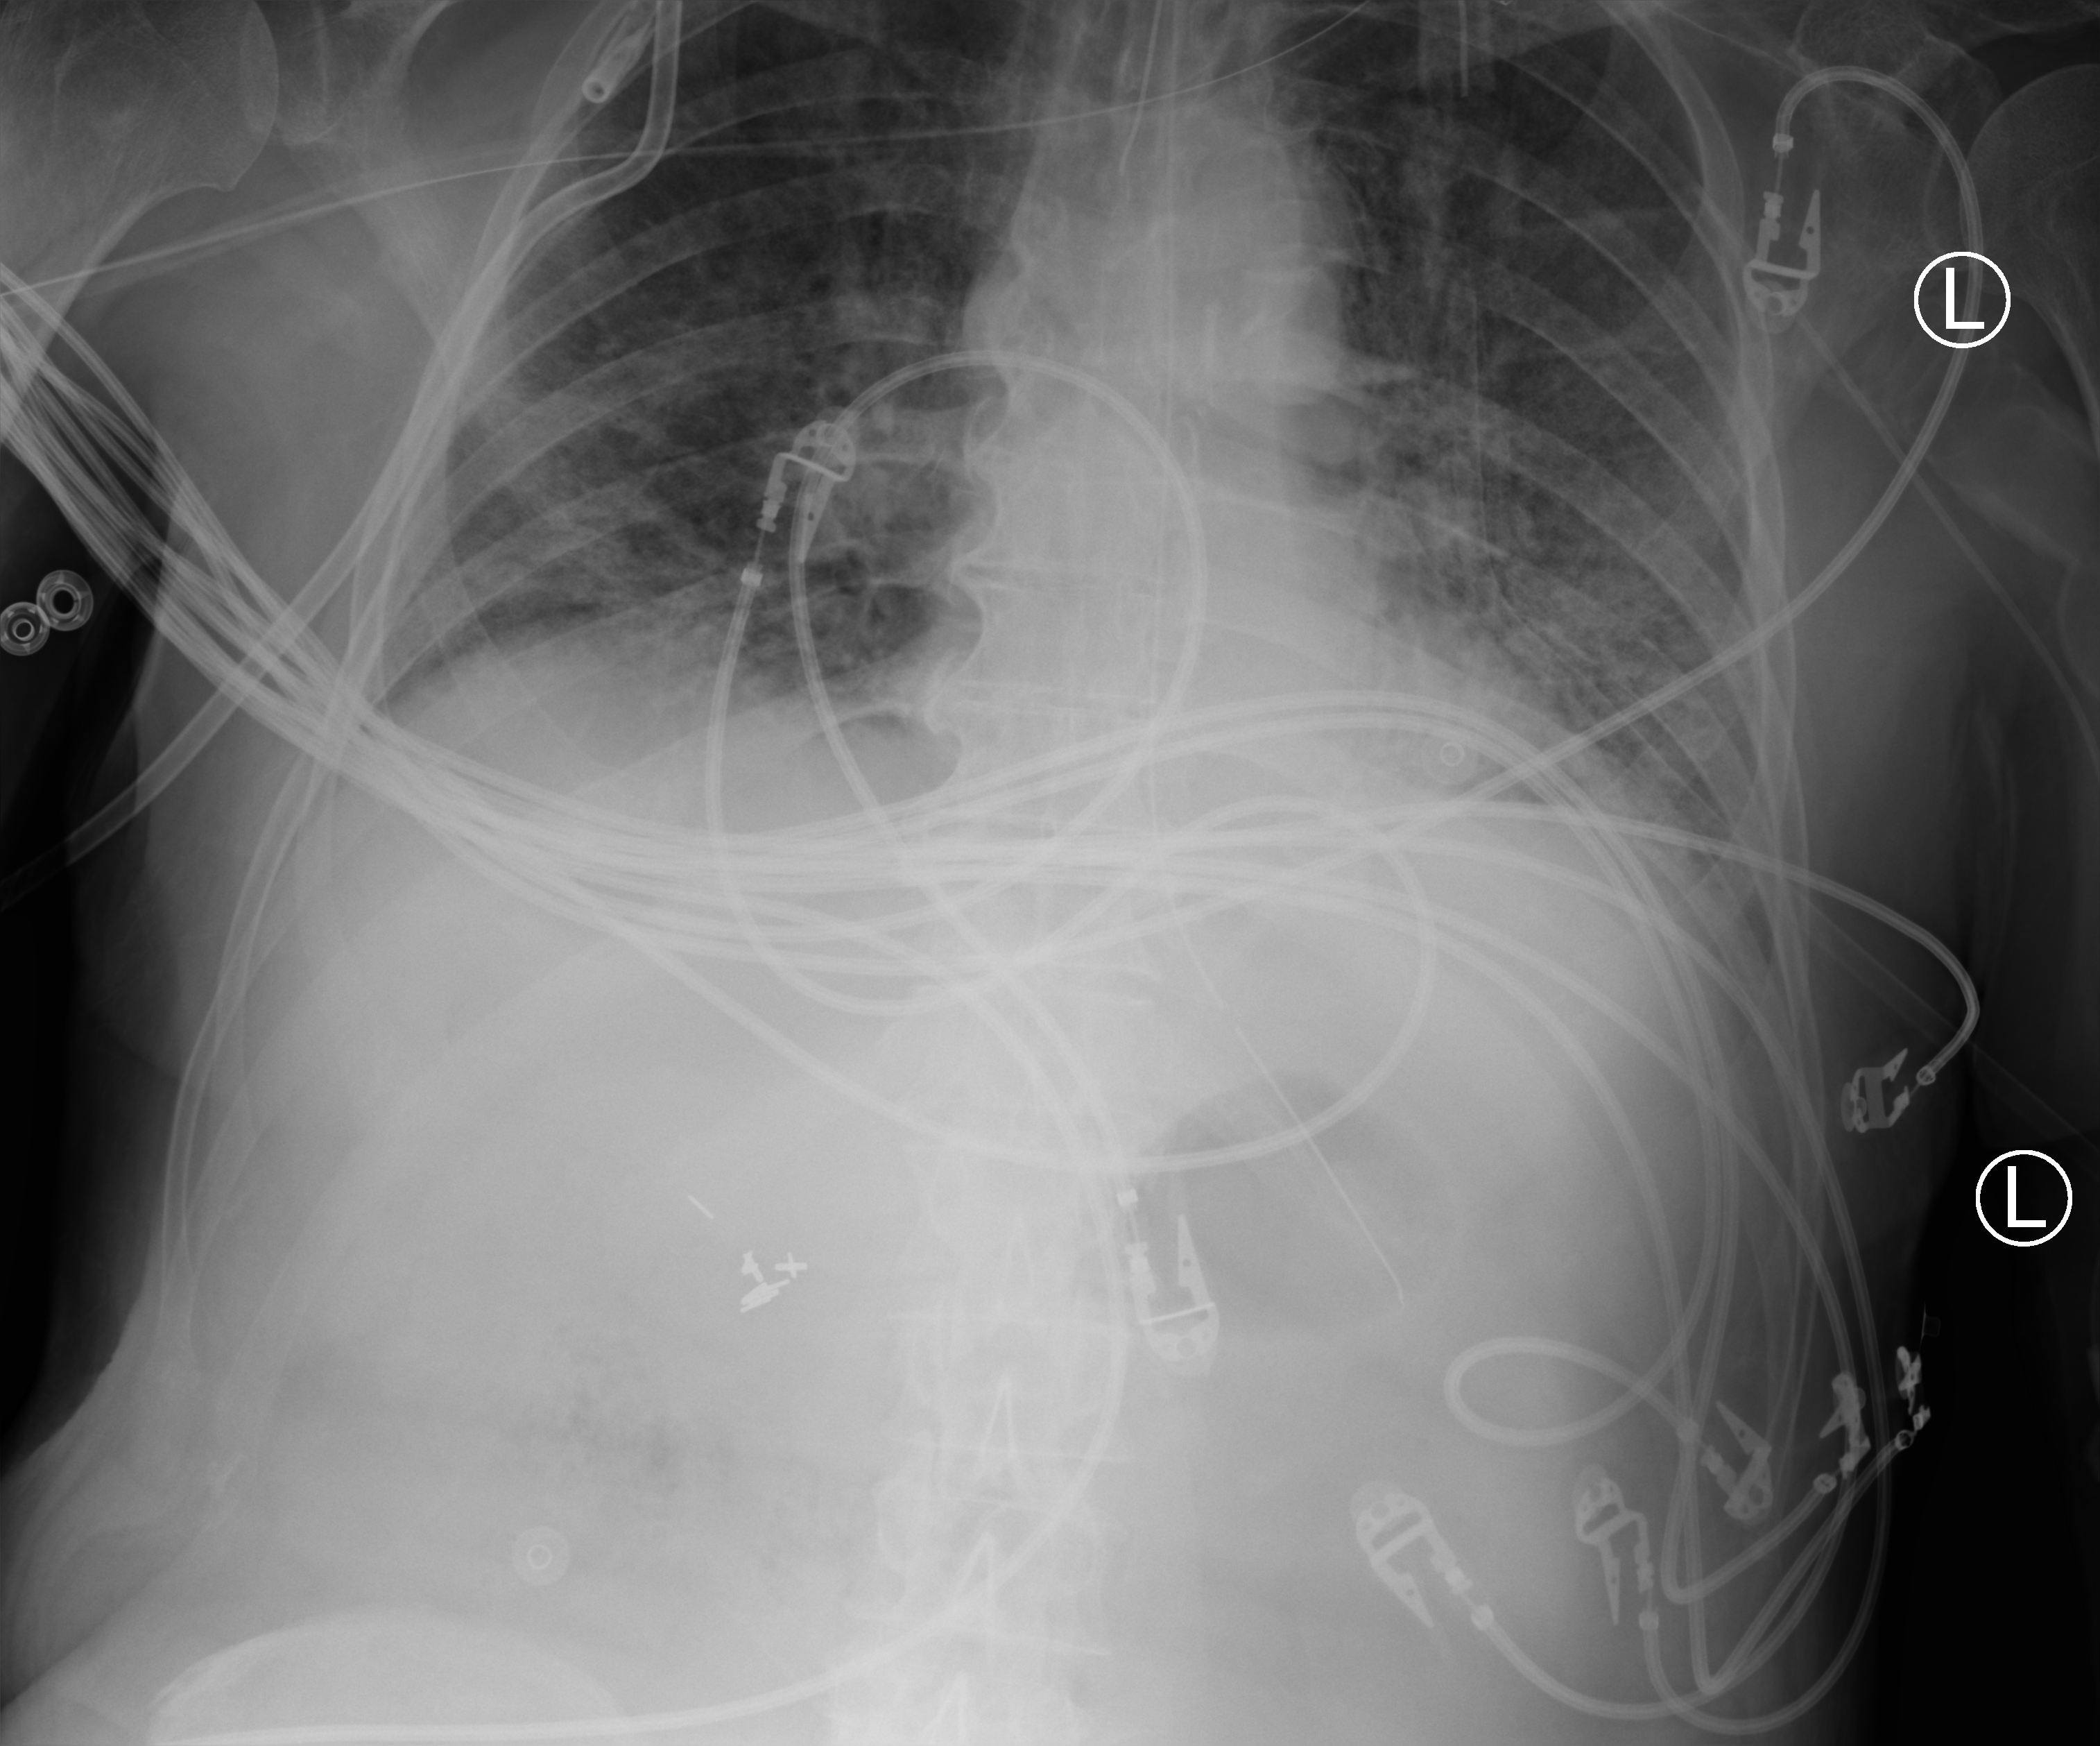
Chest X-ray (portable); anteroposterior (AP) projection. Patient hospitalised with COVID-19; male, aged 75–90 years.
Hospital-stay facts (about this admission, not read from this image; timing relative to this image not recorded): admitted to intensive care during this hospital stay: yes; smoking status (admission record): never.